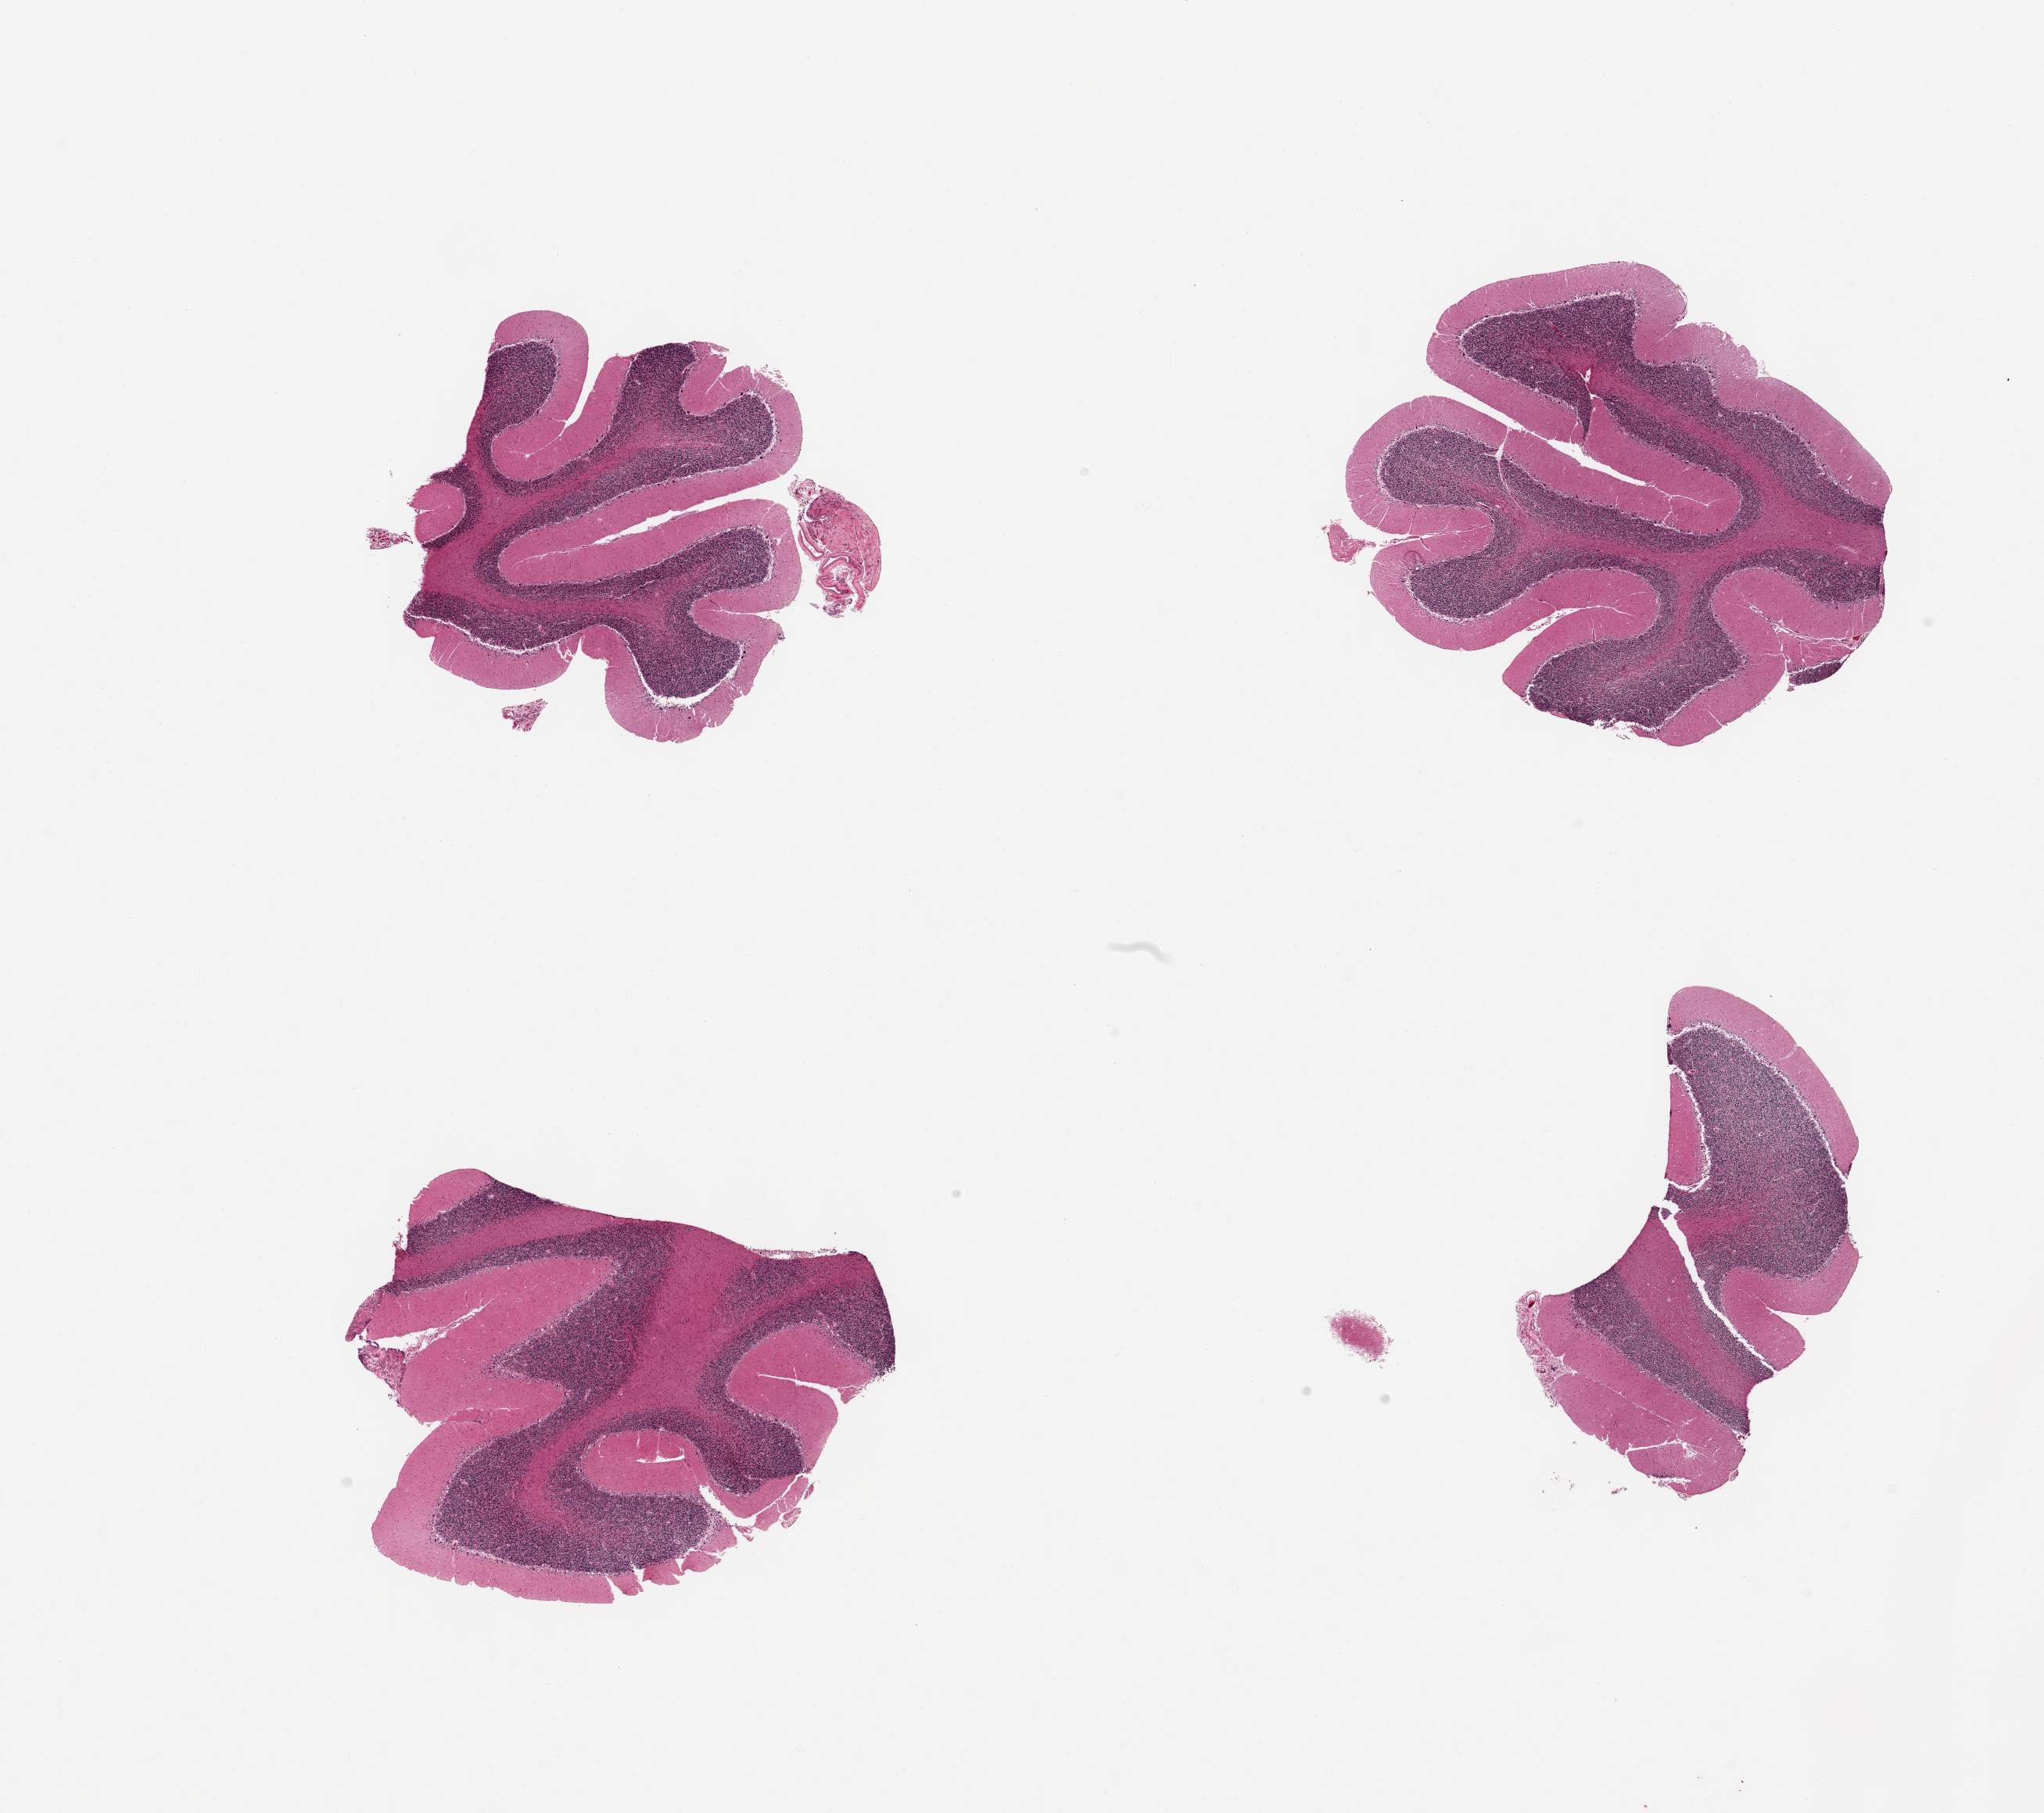
H&E whole-slide image — low-resolution overview of the scanned area, about 20.7 x 18.3 mm. PAXgene-fixed, paraffin-embedded tissue. Sampled site (target tissue): cerebellum. Donor tissue sample. Donor: male.
Review note (as recorded): 4 pieces.